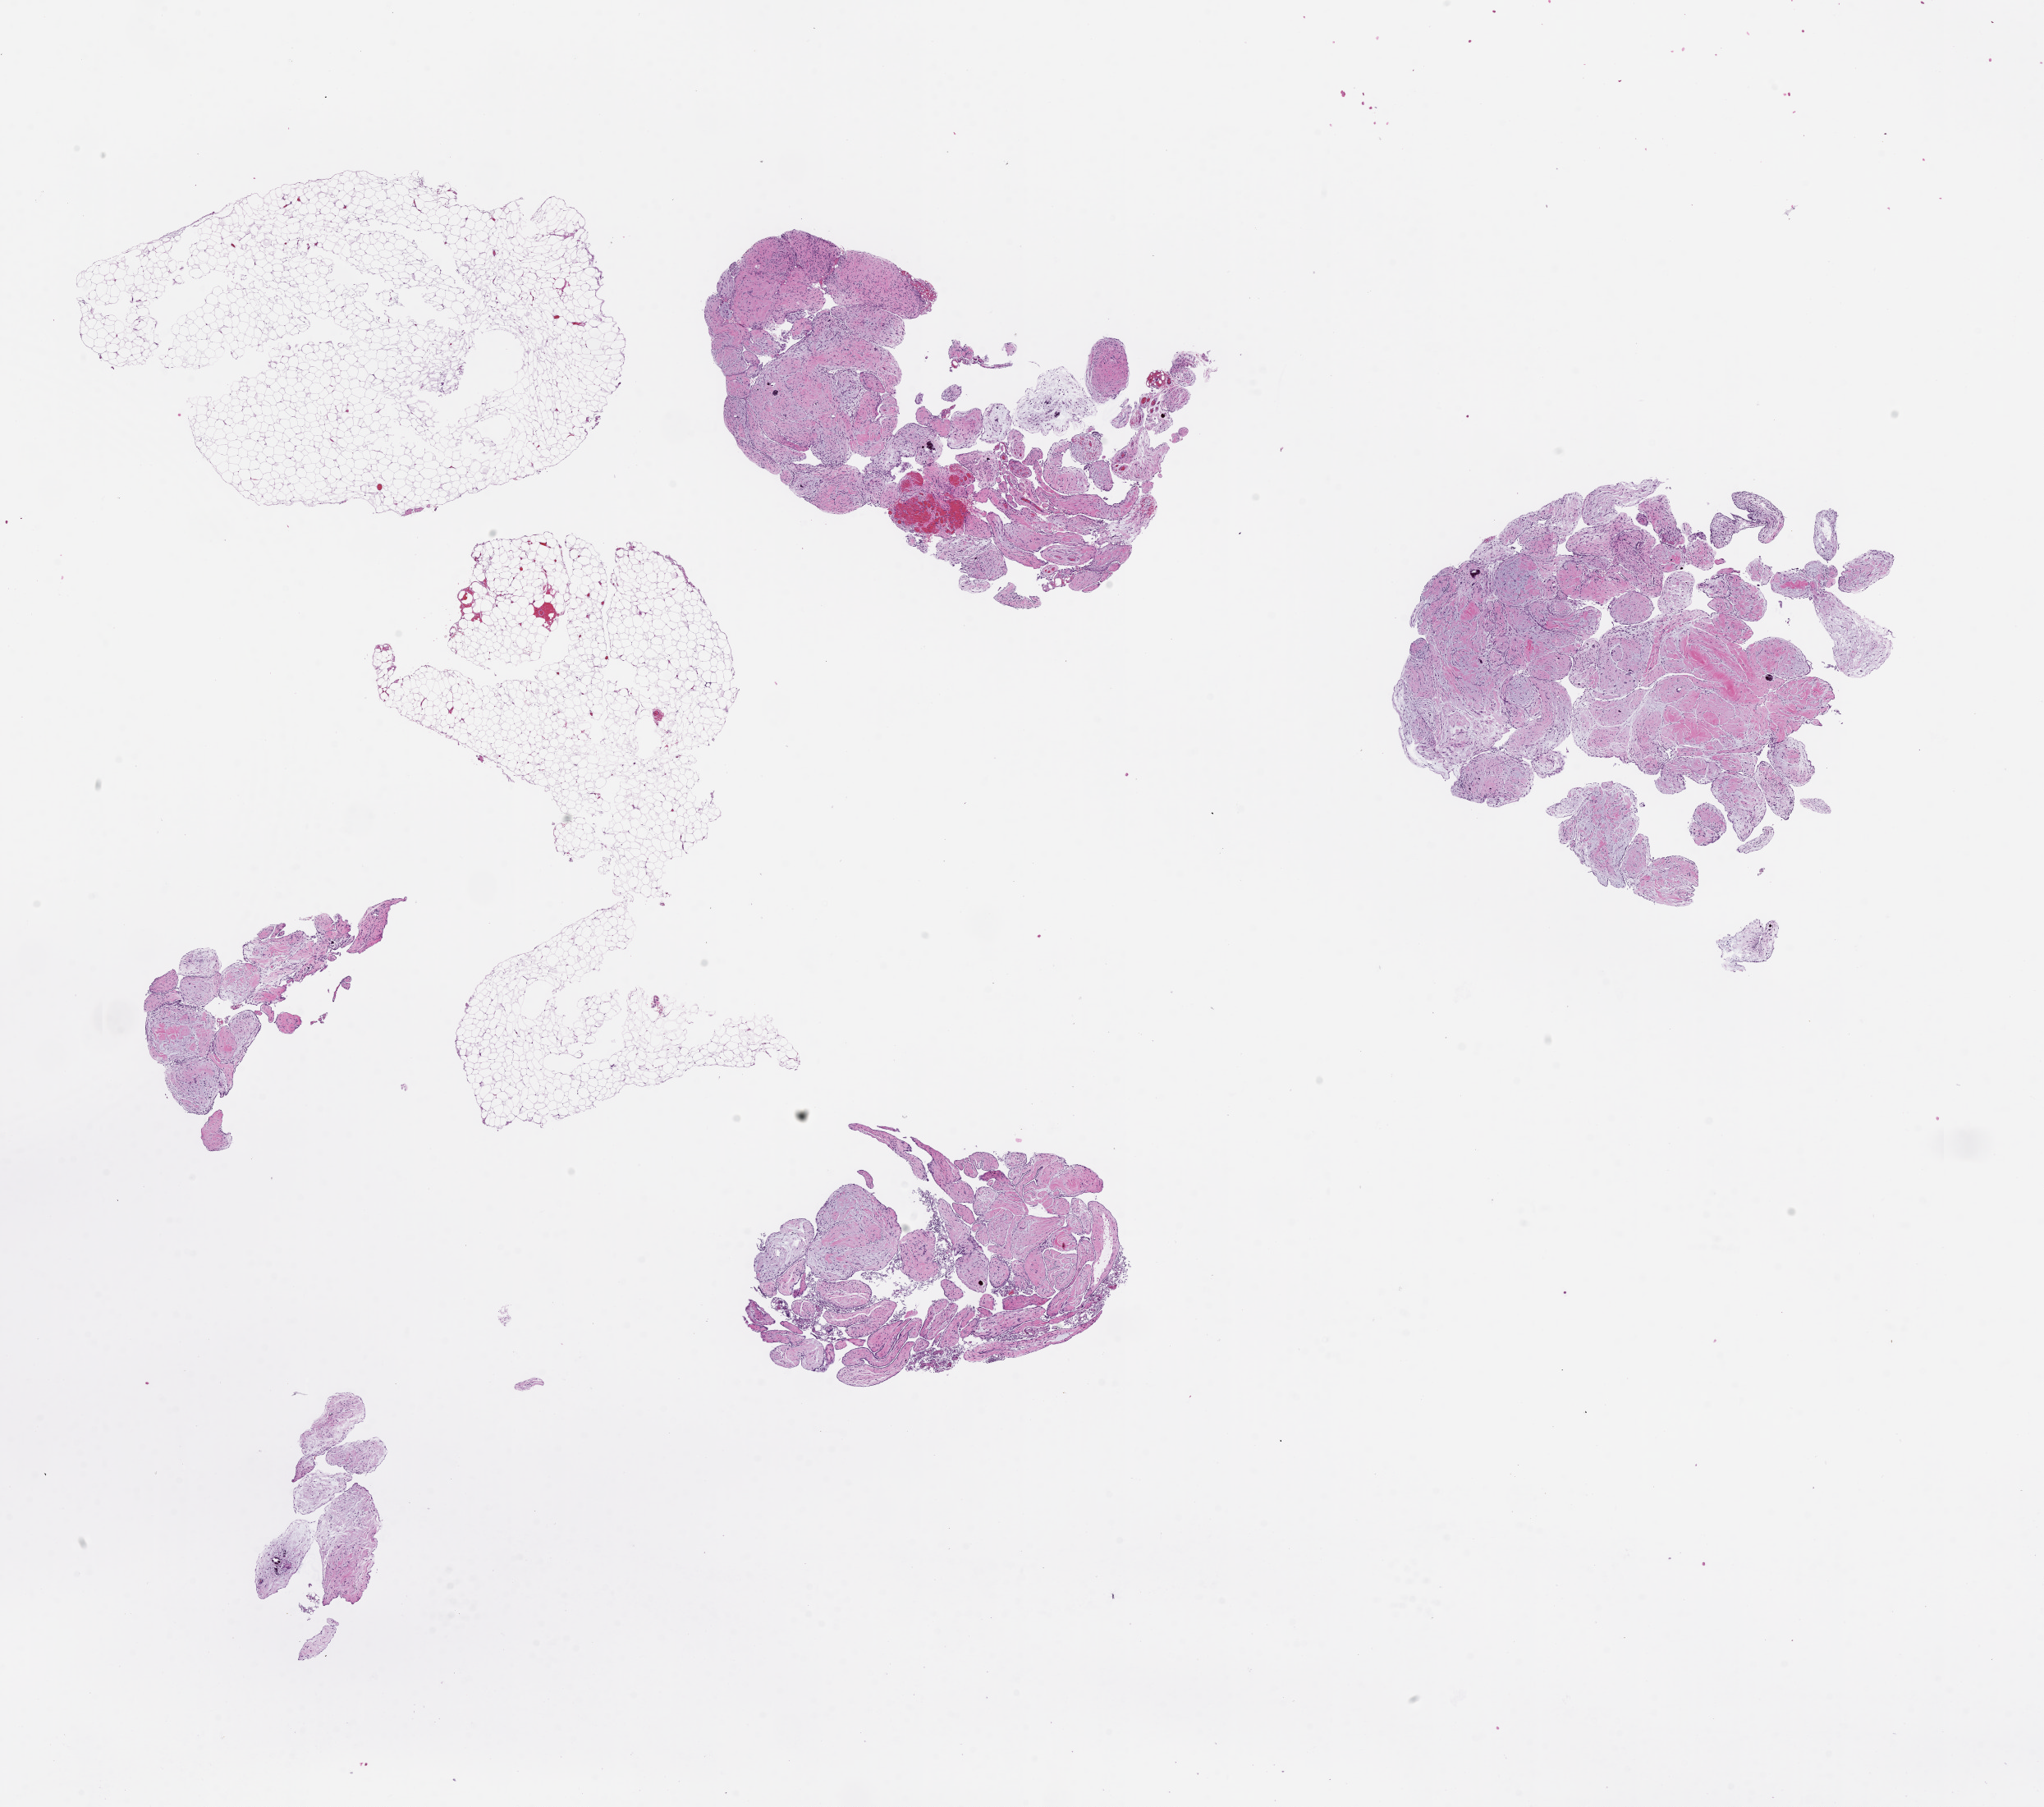
Digitized haematoxylin and eosin-stained section — a low-resolution overview of the entire scanned area, about 20.0 x 17.7 mm, FFPE section, collected on treatment. Patient: female.
* this section: metastasis (sampled organ not recorded)
* primary diagnosis of the patient: Ovarian Carcinoma